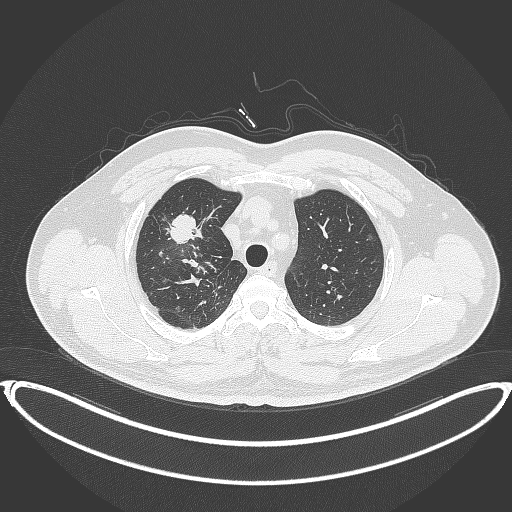
Chest CT, one axial slice; slice 308 of 399 in the series (ordered by position); reconstruction kernel B70f; 120 kVp; lung window (W 1500 / L -600 HU); 1 mm slice thickness; 512 × 512 image matrix, field of view 445 × 445 mm. Male patient, age 53 years. From the clinical record (not read from this slice): clinical TNM (as recorded): T2a N0 M0.
Structures marked on this image (bounding box drawn by a radiologist):
- lung tumour (recorded histology: adenocarcinoma): bounding box (x1, y1, x2, y2) in pixels: (163, 212, 202, 248)